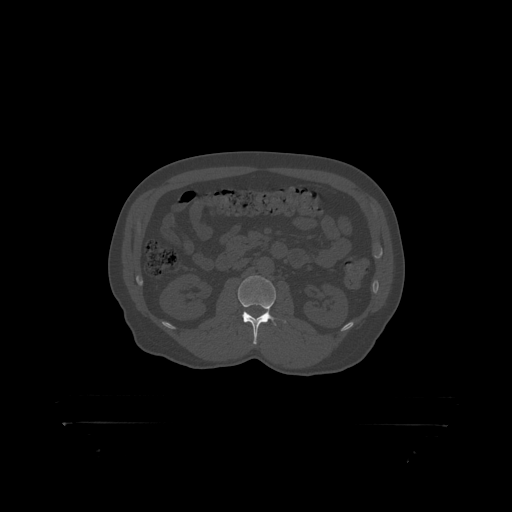
CT including the spine, one axial slice; slice 293 of 399 in the series (ordered by position); 120 kVp; bone window (W 1800 / L 400 HU); 1.25 mm slice thickness; 512 × 512 image matrix, field of view 650 × 650 mm. Male patient, age 46 years. Case-level facts recorded for this patient, not image findings: primary cancer: skin.
Structures marked on this image (semi-automatic segmentation, software-assisted and operator-edited):
- L2 vertebra: bounding box <238,276,277,319> (left, top, right, bottom; pixels)